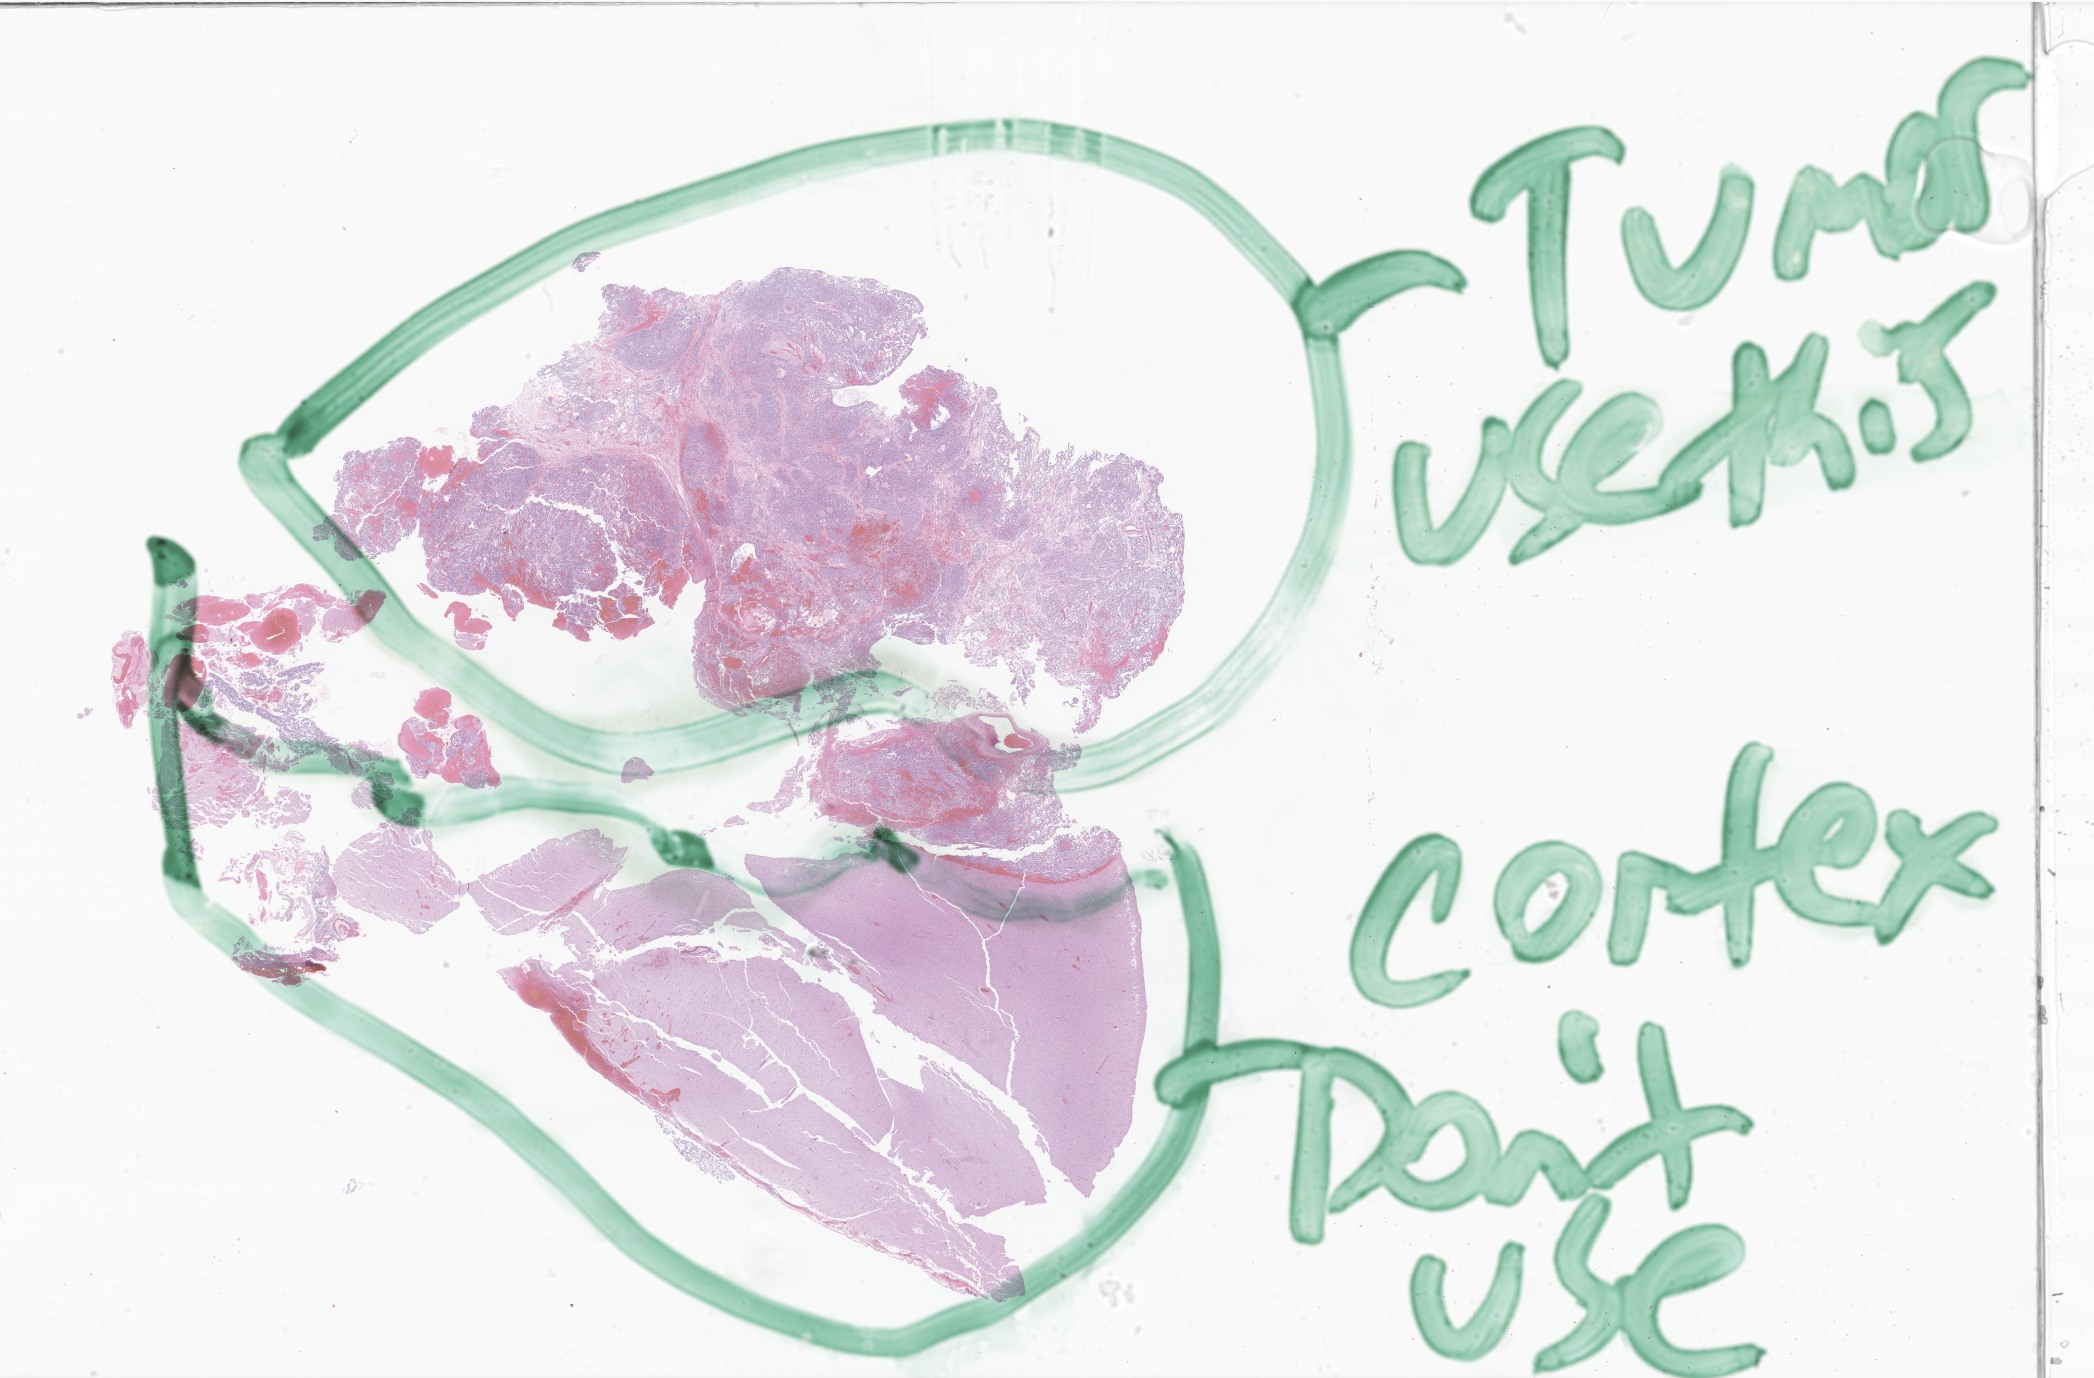
Digitized hematoxylin and eosin (H&E)-stained section of tumor tissue from the brain — shown as a low-resolution overview of the whole scanned area (about 35.3 x 23.2 mm). FFPE section. Patient female; age 130 months (10 years 10 months).
Diagnosis (ICD-O-3 morphology term): Neoplasm, malignant.